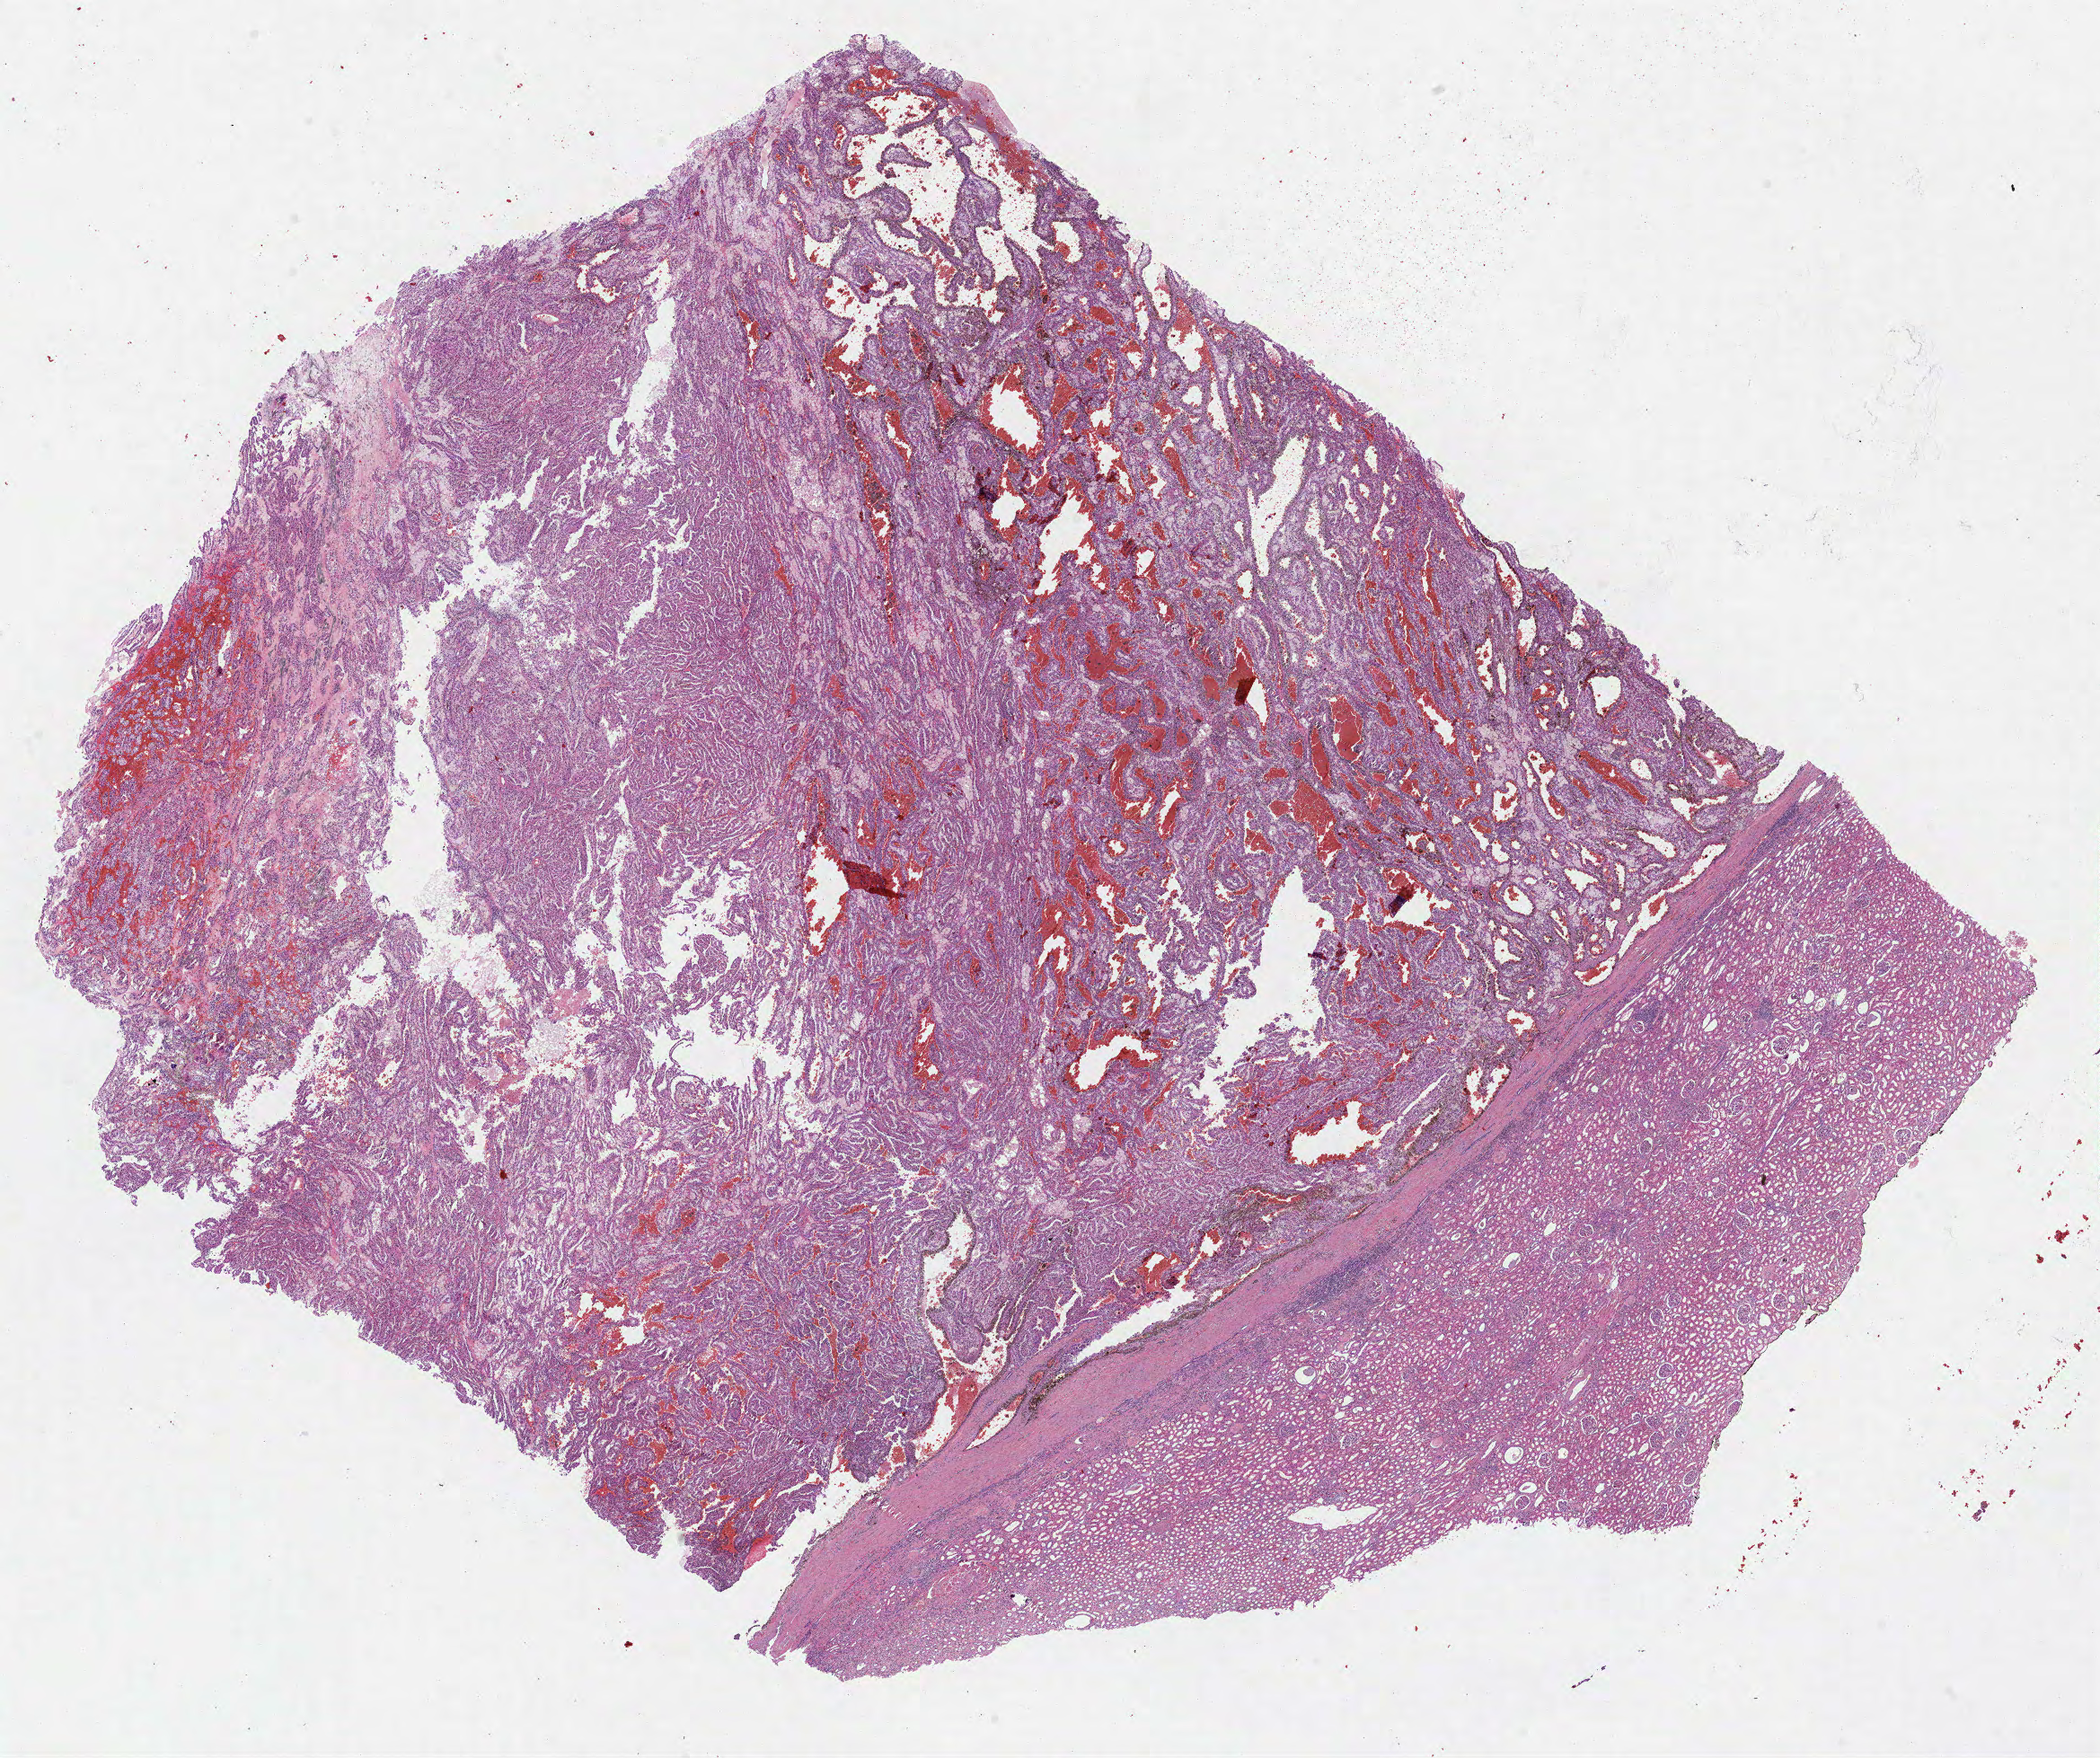
Digitized H&E-stained tissue section (whole slide) — shown as a low-resolution overview of the whole scanned area (about 18.9 x 15.8 mm, from a 40x scan); FFPE section; kidney, primary tumour sample. Patient: female, age at initial diagnosis 59 years.
Diagnosis: Papillary adenocarcinoma, NOS. TNM: T1b NX MX. AJCC pathologic stage: I (7th edition).